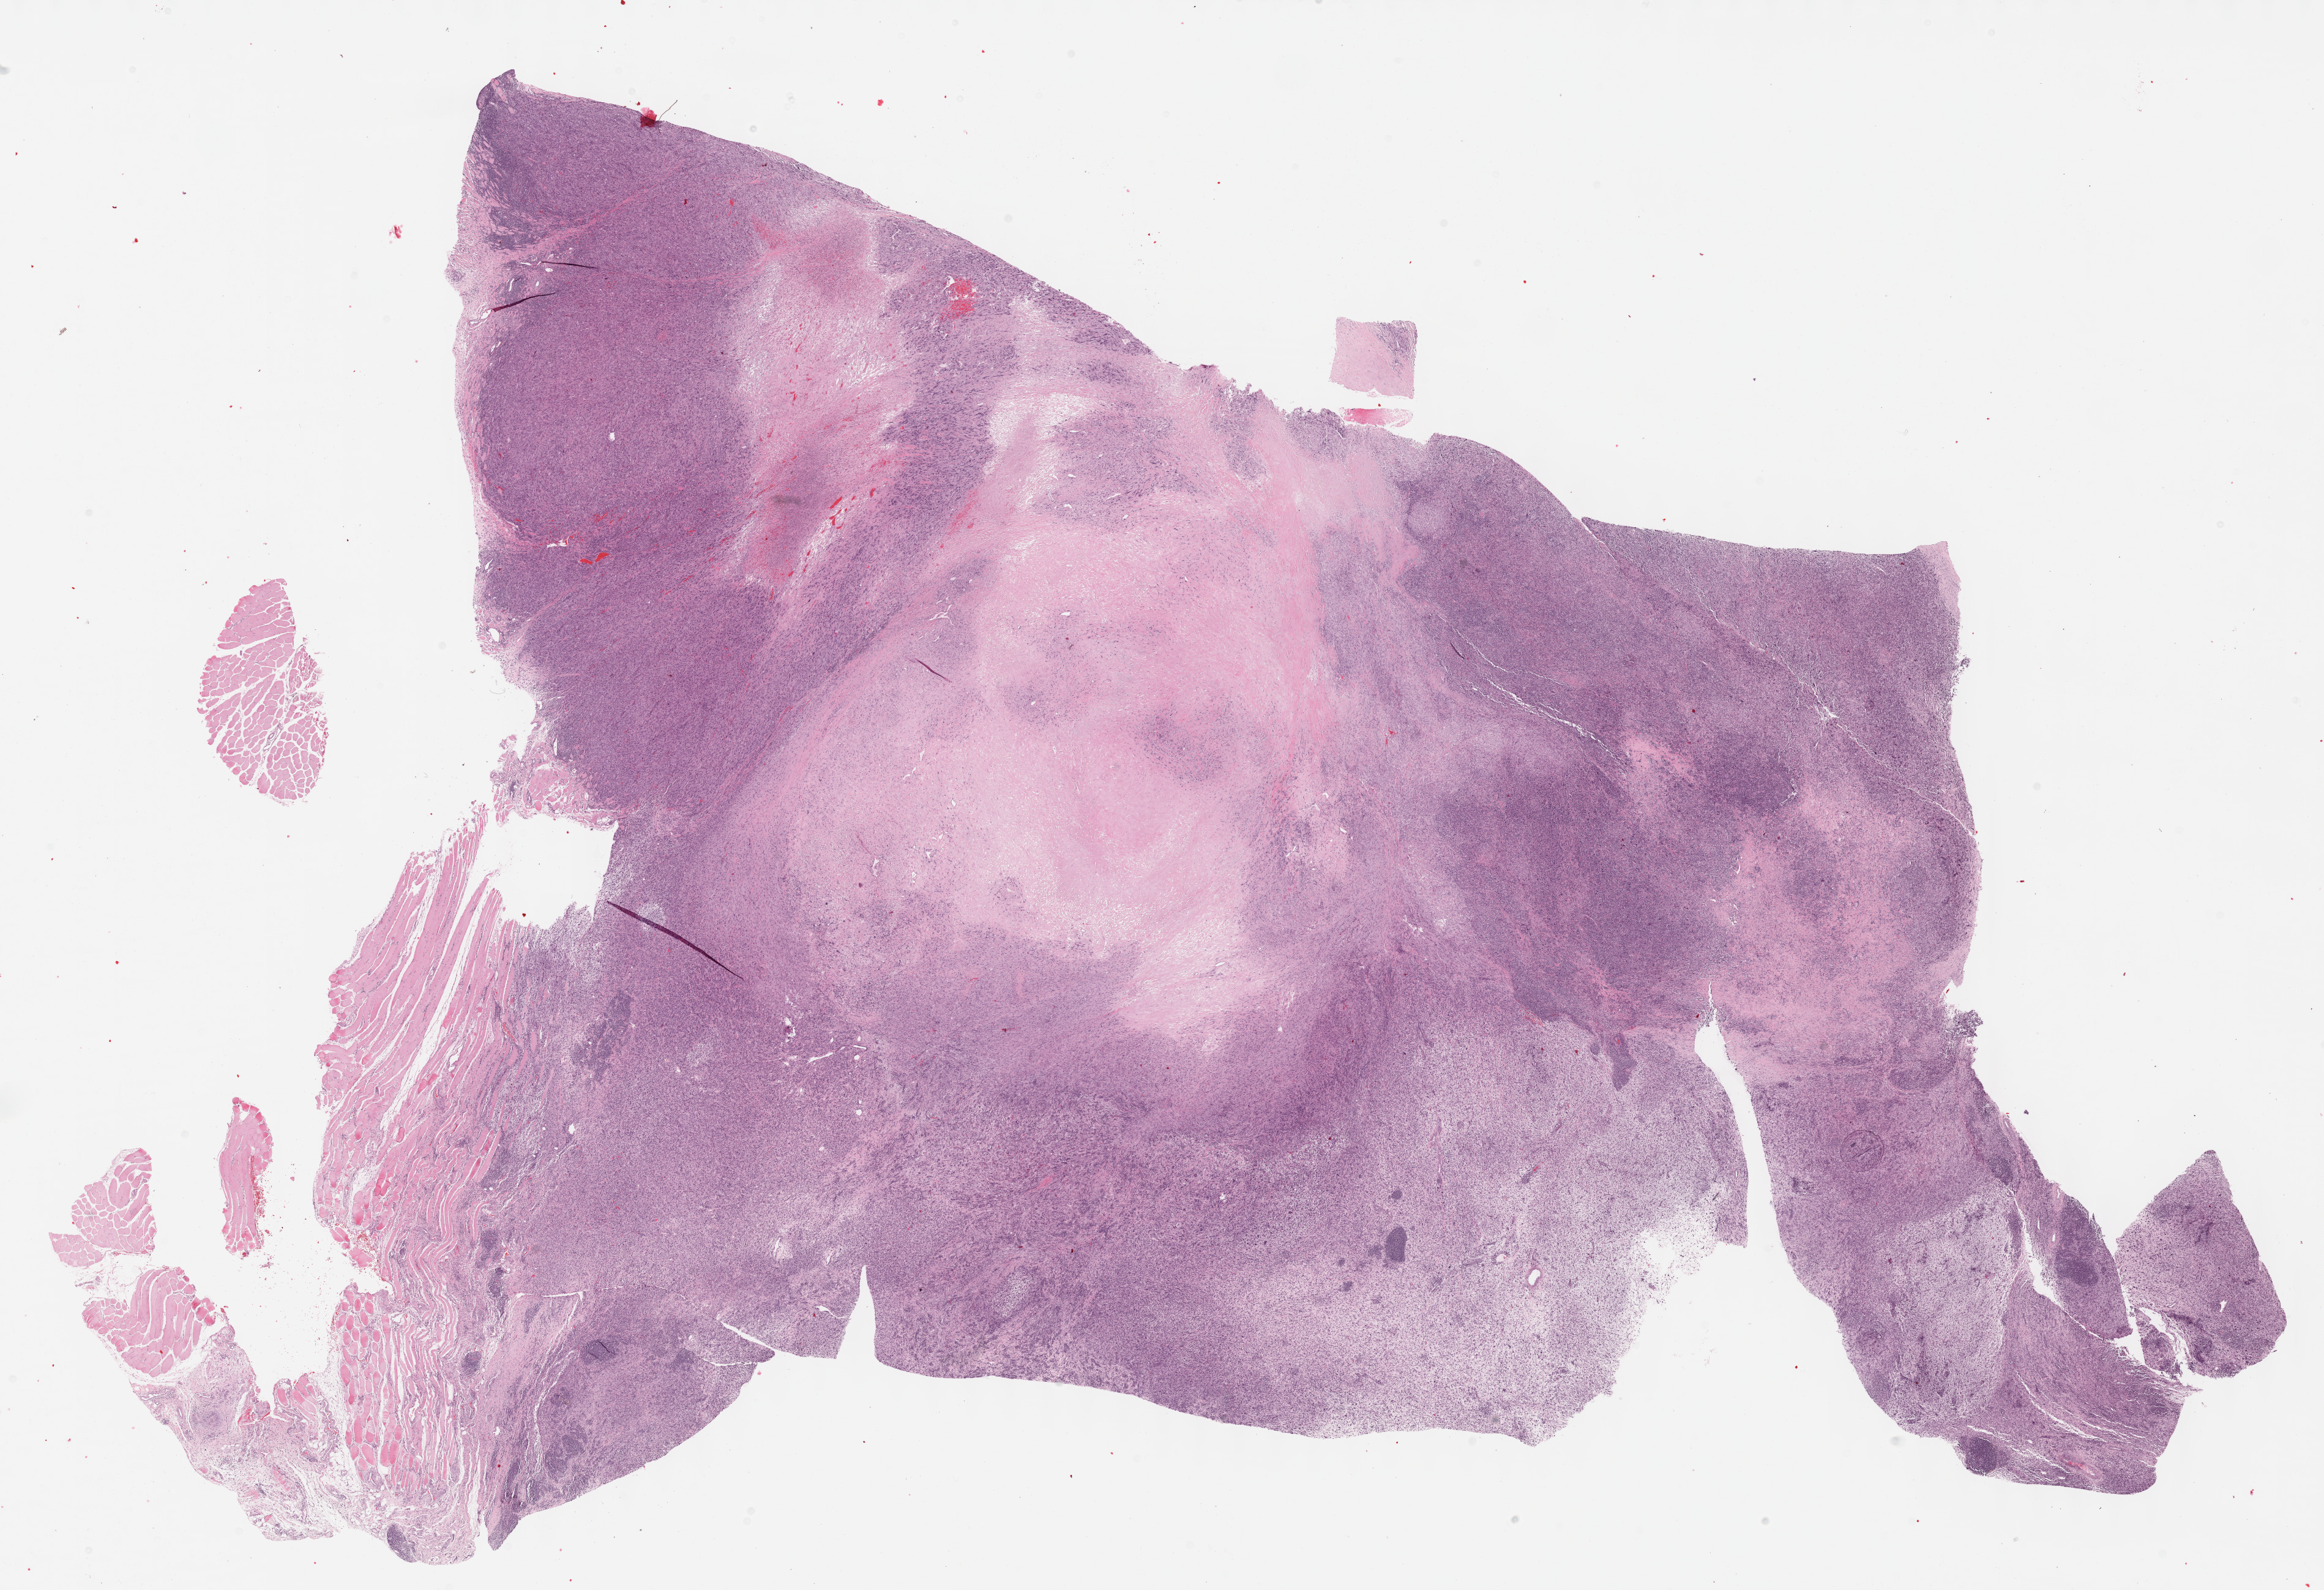
Whole-slide histology image, Hematoxylin and eosin (H&E) stained, whole scanned area (about 30.7 x 21.0 mm) shown as a low-resolution overview, FFPE section, primary tumour sample from the connective, subcutaneous and other soft tissues. Male, age 59 years at initial diagnosis.
Histologic diagnosis: Undifferentiated sarcoma (connective, subcutaneous and other soft tissues of upper limb and shoulder).